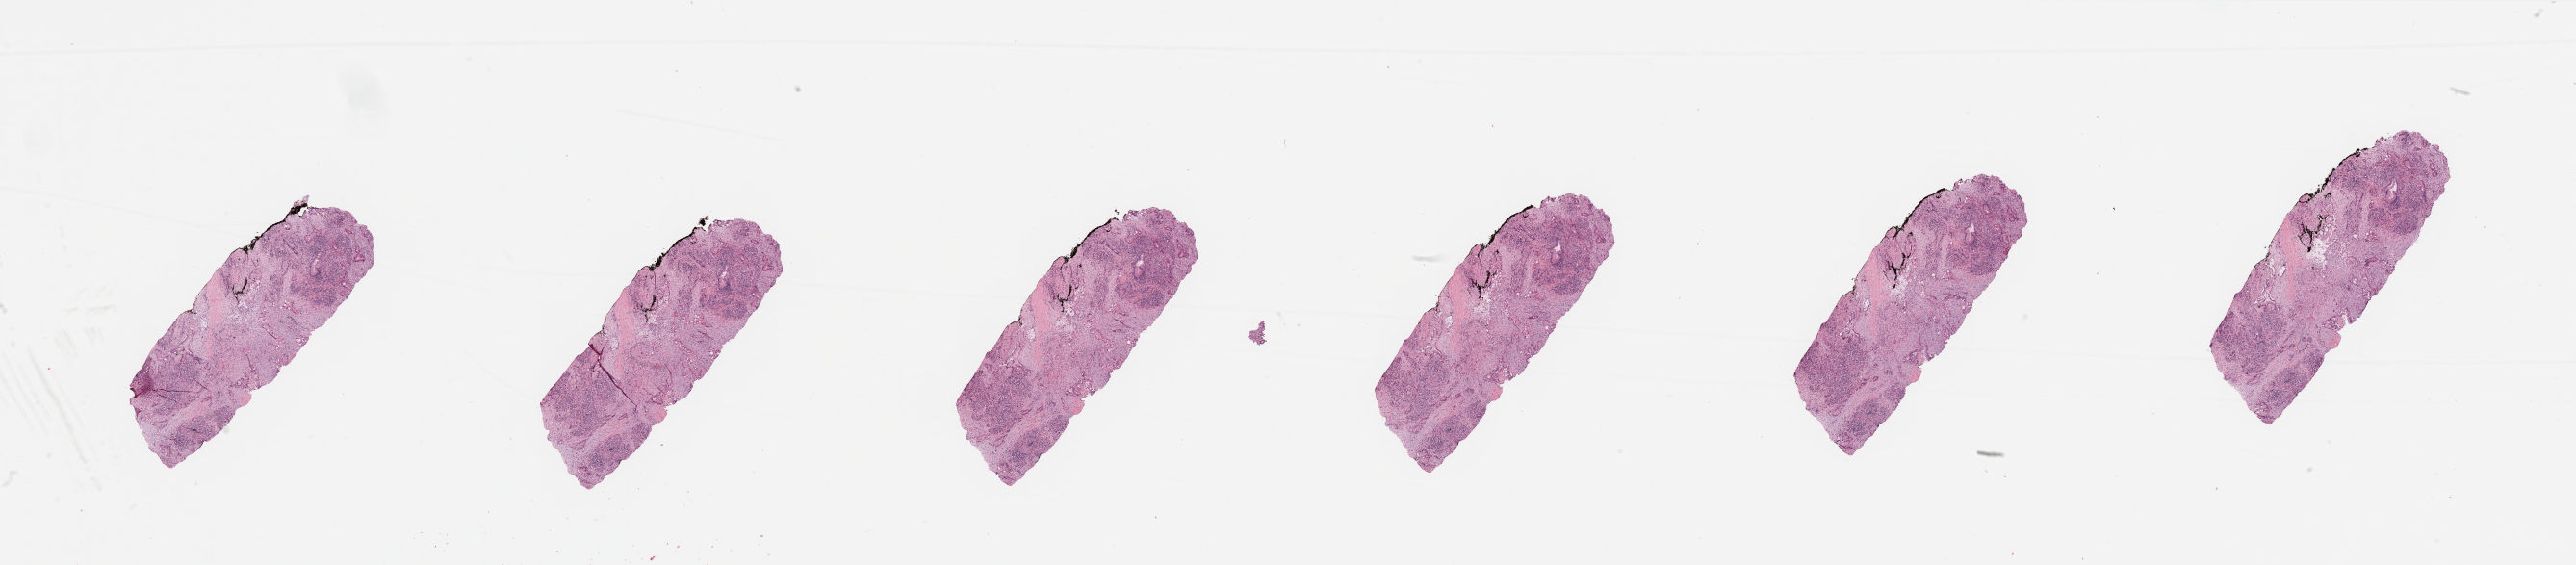
H&E-stained whole-slide image, a low-resolution overview of the entire scanned area, about 42.3 x 9.3 mm, pancreas, tumour tissue. Female, 69 y/o. Histologic grade: G2 (moderately differentiated).
• histologic diagnosis: Infiltrating duct carcinoma, NOS
• AJCC pathologic stage: IIB